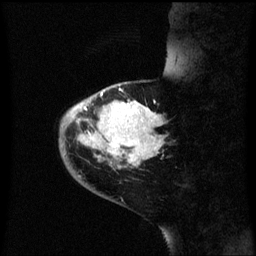
Breast MRI (dynamic contrast-enhanced), one sagittal slice; slice 16 of 60 in the series (ordered by position); dynamic contrast-enhanced series, image 2 of 3 at this slice position (ordered by acquisition); 1.5 T; TE 4.2 ms, TR 8.4 ms; 256 × 256 image matrix, field of view 200 × 200 mm. Female patient, age 46 years. Case-level facts recorded for this patient, not image findings: setting: breast cancer imaged before/during neoadjuvant chemotherapy; receptor status: HER2-positive.
Outlined on this slice (semi-automatic segmentation, software-assisted and operator-edited):
- analysis volume of interest (the breast-tissue region the enhancement analysis was run in; not a lesion): box from (x=60, y=86) to (x=165, y=171) px
- tumour enhancement mask (voxels above the 70 % enhancement threshold inside the analysis volume of interest): (x=72, y=92)–(x=163, y=167)